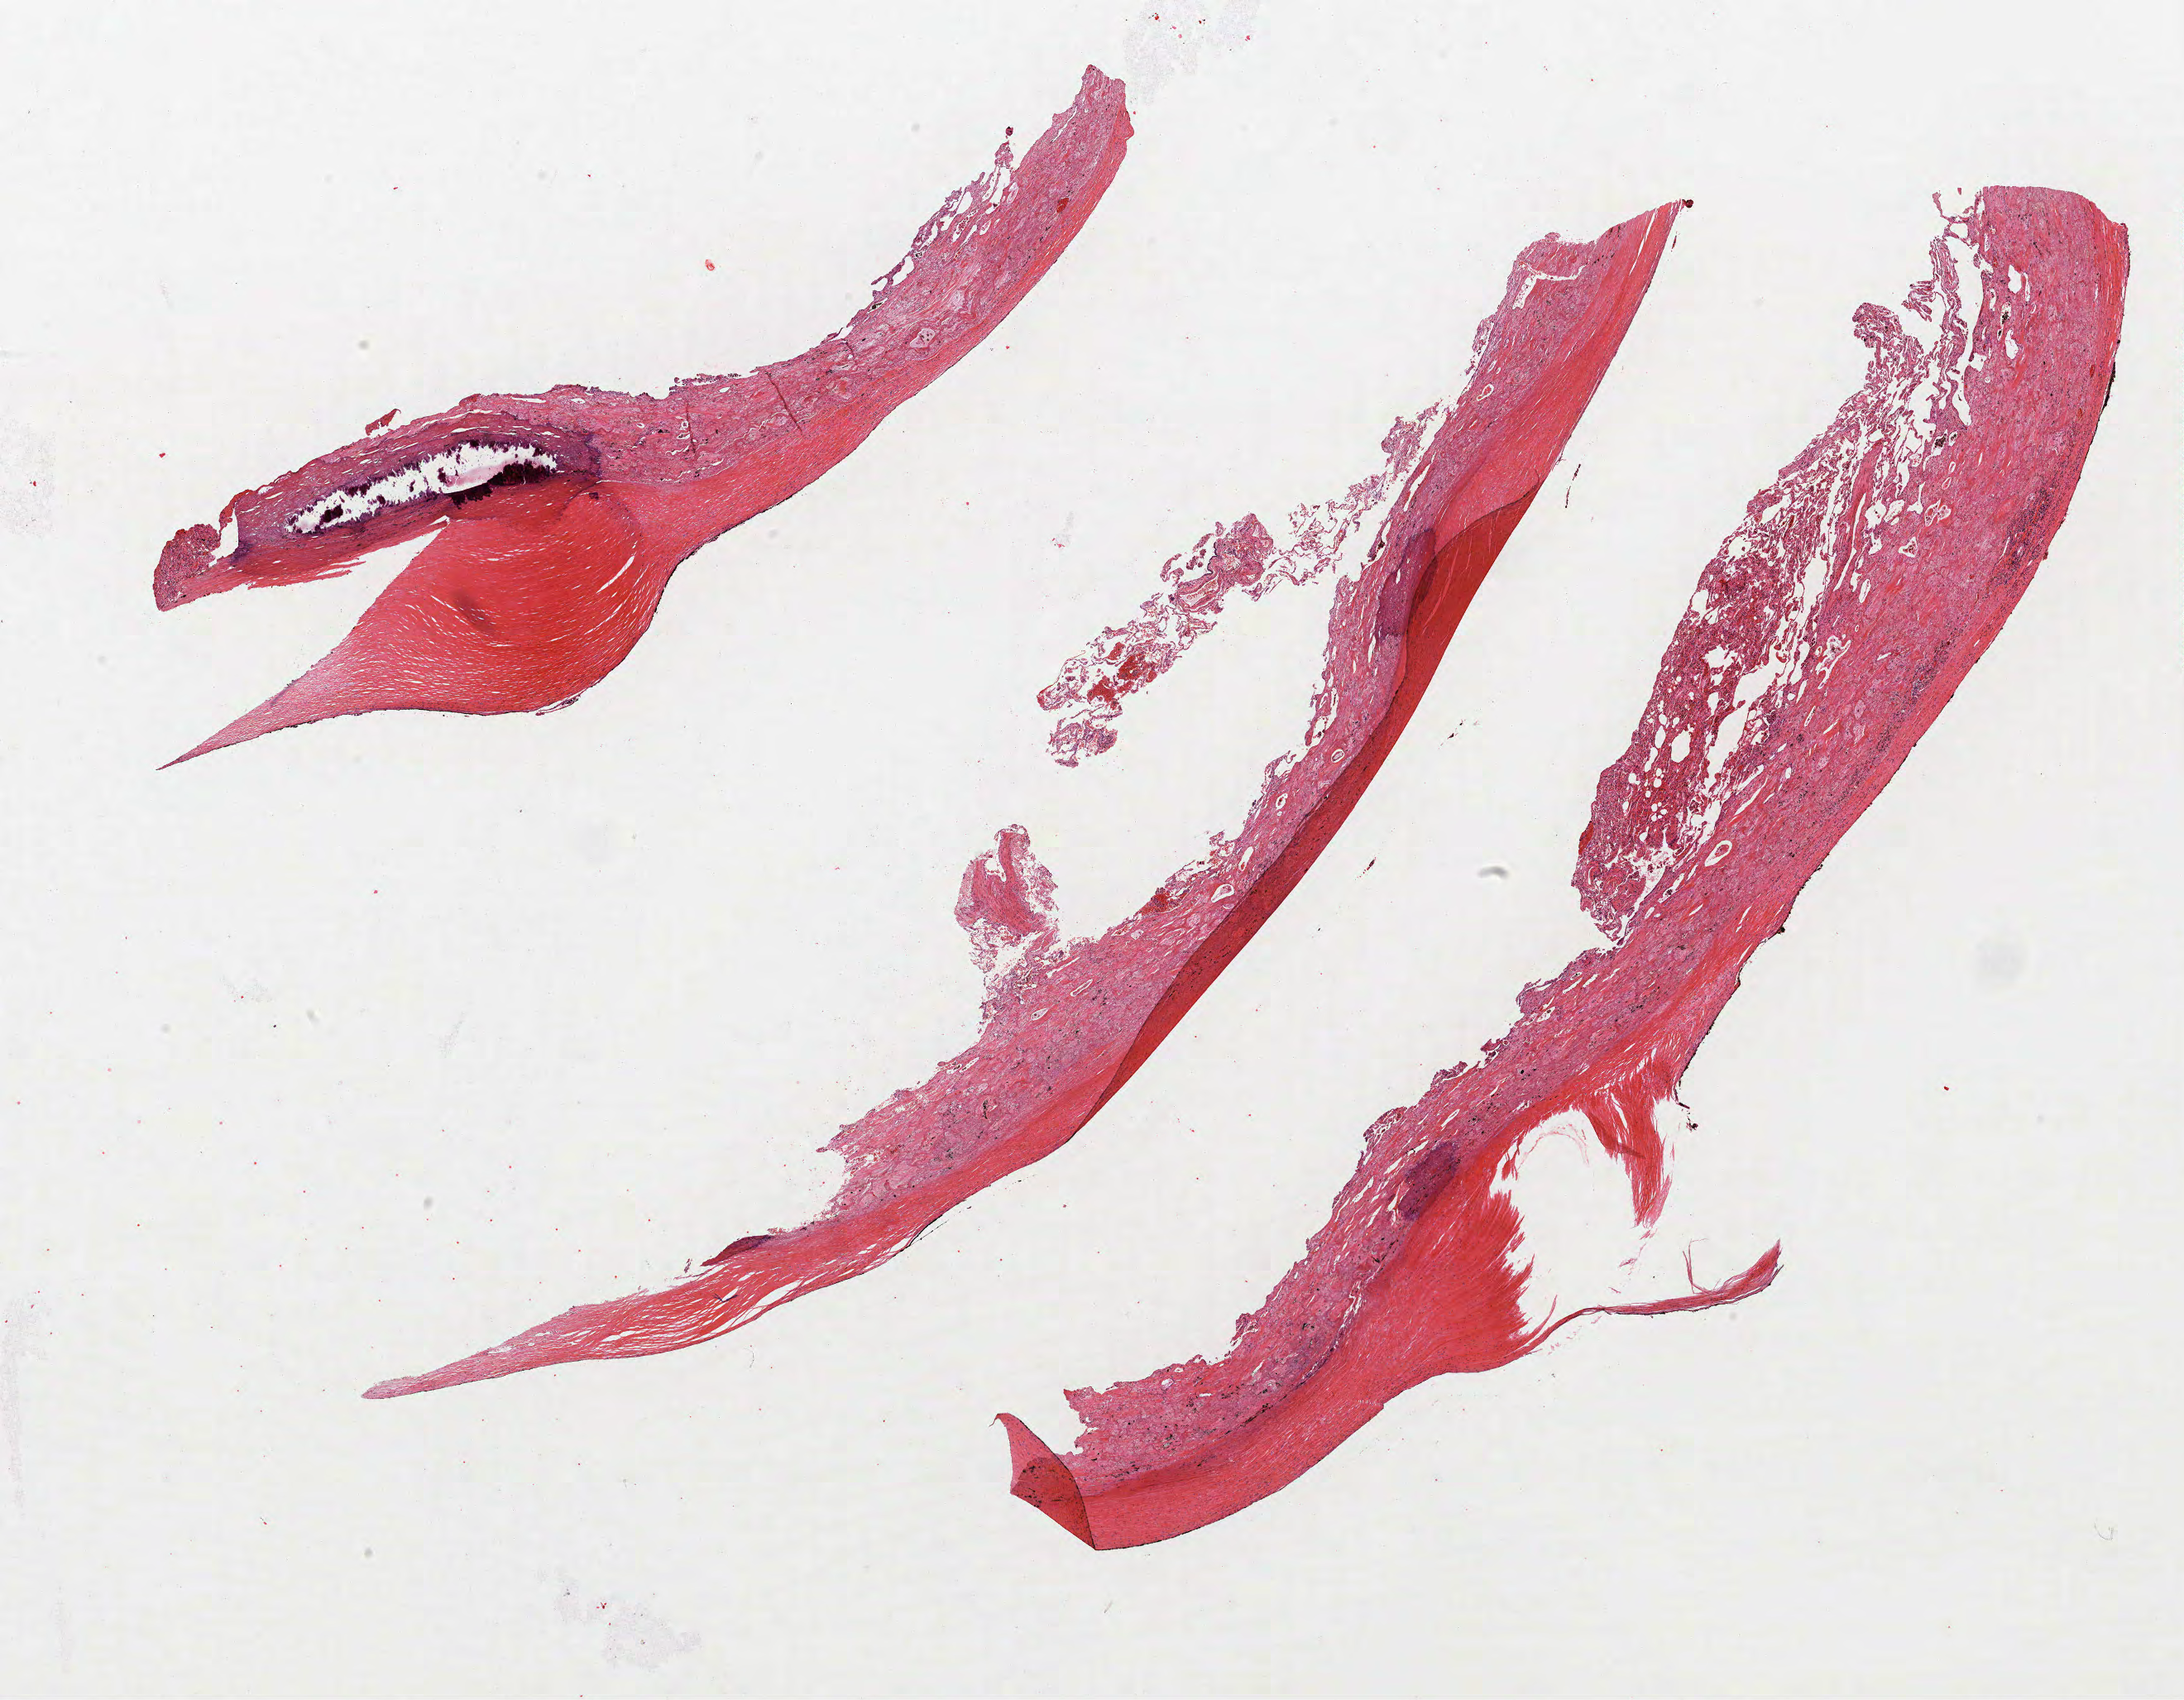
Whole-slide histology image, H&E-stained — low-resolution overview of the scanned area, about 21.1 x 16.4 mm. Formalin-fixed paraffin-embedded (FFPE) section. Lung. Male patient, aged 57 at enrolment. Current smoker at enrolment. Grade: well differentiated (G1).
- participant's lung-cancer diagnosis: Adenocarcinoma, NOS (ICD-O-3 8140/3)
- primary tumour location (clinical record): left upper lobe
- tumour size (pathology): 30 mm
- stage (AJCC 6th edition): IA
- ICD-O-3 topography: upper lobe of lung (C34.1)